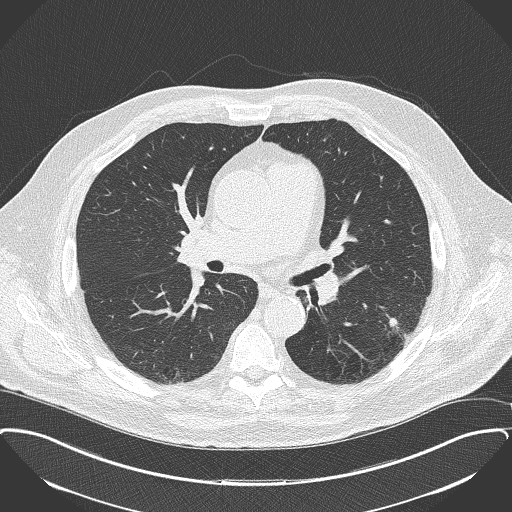
Axial slice from a low-dose chest CT screening exam, second annual screen, lung window (W 1500 / L -600 HU), 2 mm slice thickness, slice 77 of 175 in the series, 512 × 512 image matrix, field of view 400 × 400 mm. Male participant, aged 68 years at enrolment.
• Lesion marked by an expert reader, bounding box [x1, y1, x2, y2] px = [375, 294, 432, 346].
• The screening reader recorded 2 non-calcified nodules or masses ≥4 mm on this exam (left lower lobe, left lower lobe); which of them this box marks is not recorded.